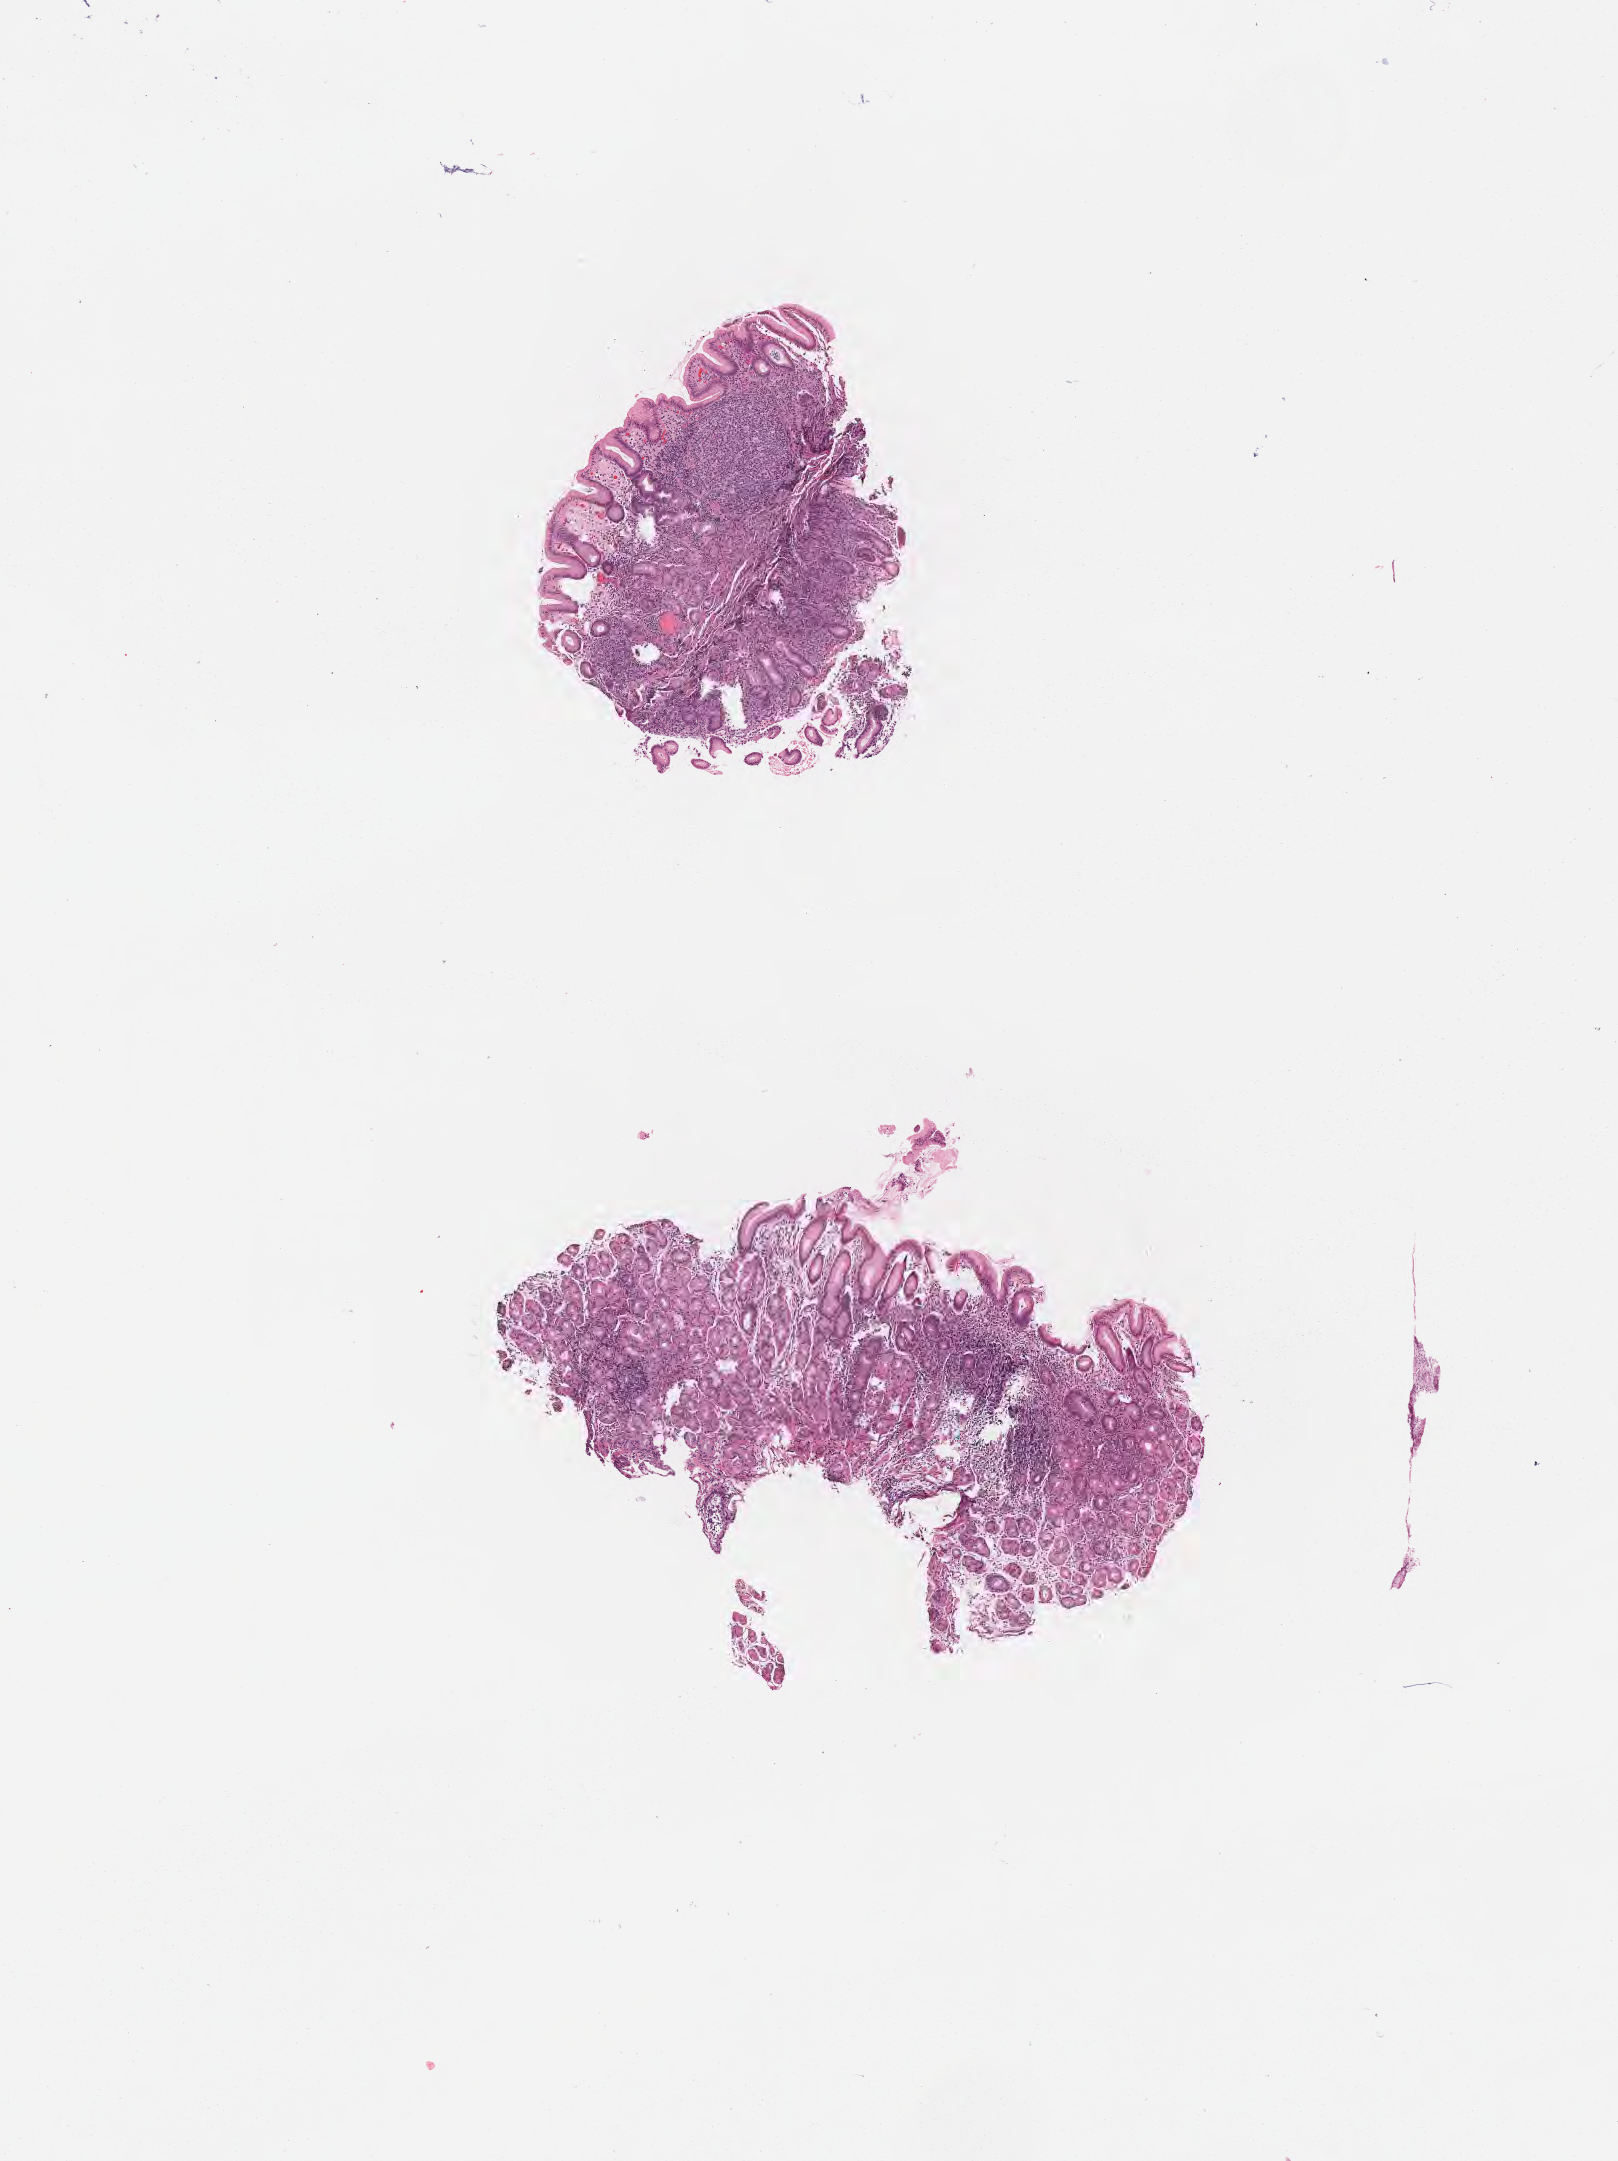
Digitized H&E-stained section — low-resolution overview of the scanned area, about 6.5 x 8.7 mm. Formalin-fixed, paraffin-embedded (FFPE) tissue. Non-tumor (normal tissue) sample from a patient with burkitt lymphoma, NOS. Male patient, age 36 years. Pathologist review of this section (percent, as recorded): tumor cells 0%, tumor nuclei 0%, stromal cells 0%, necrosis 0%, normal cells 100%. Infiltration values recorded for this section: lymphocyte infiltration 60%, monocyte infiltration 10%, neutrophil infiltration 10%.
- this section: non-tumor tissue sample; the patient's diagnosis is given above
- section: top of the tissue portion